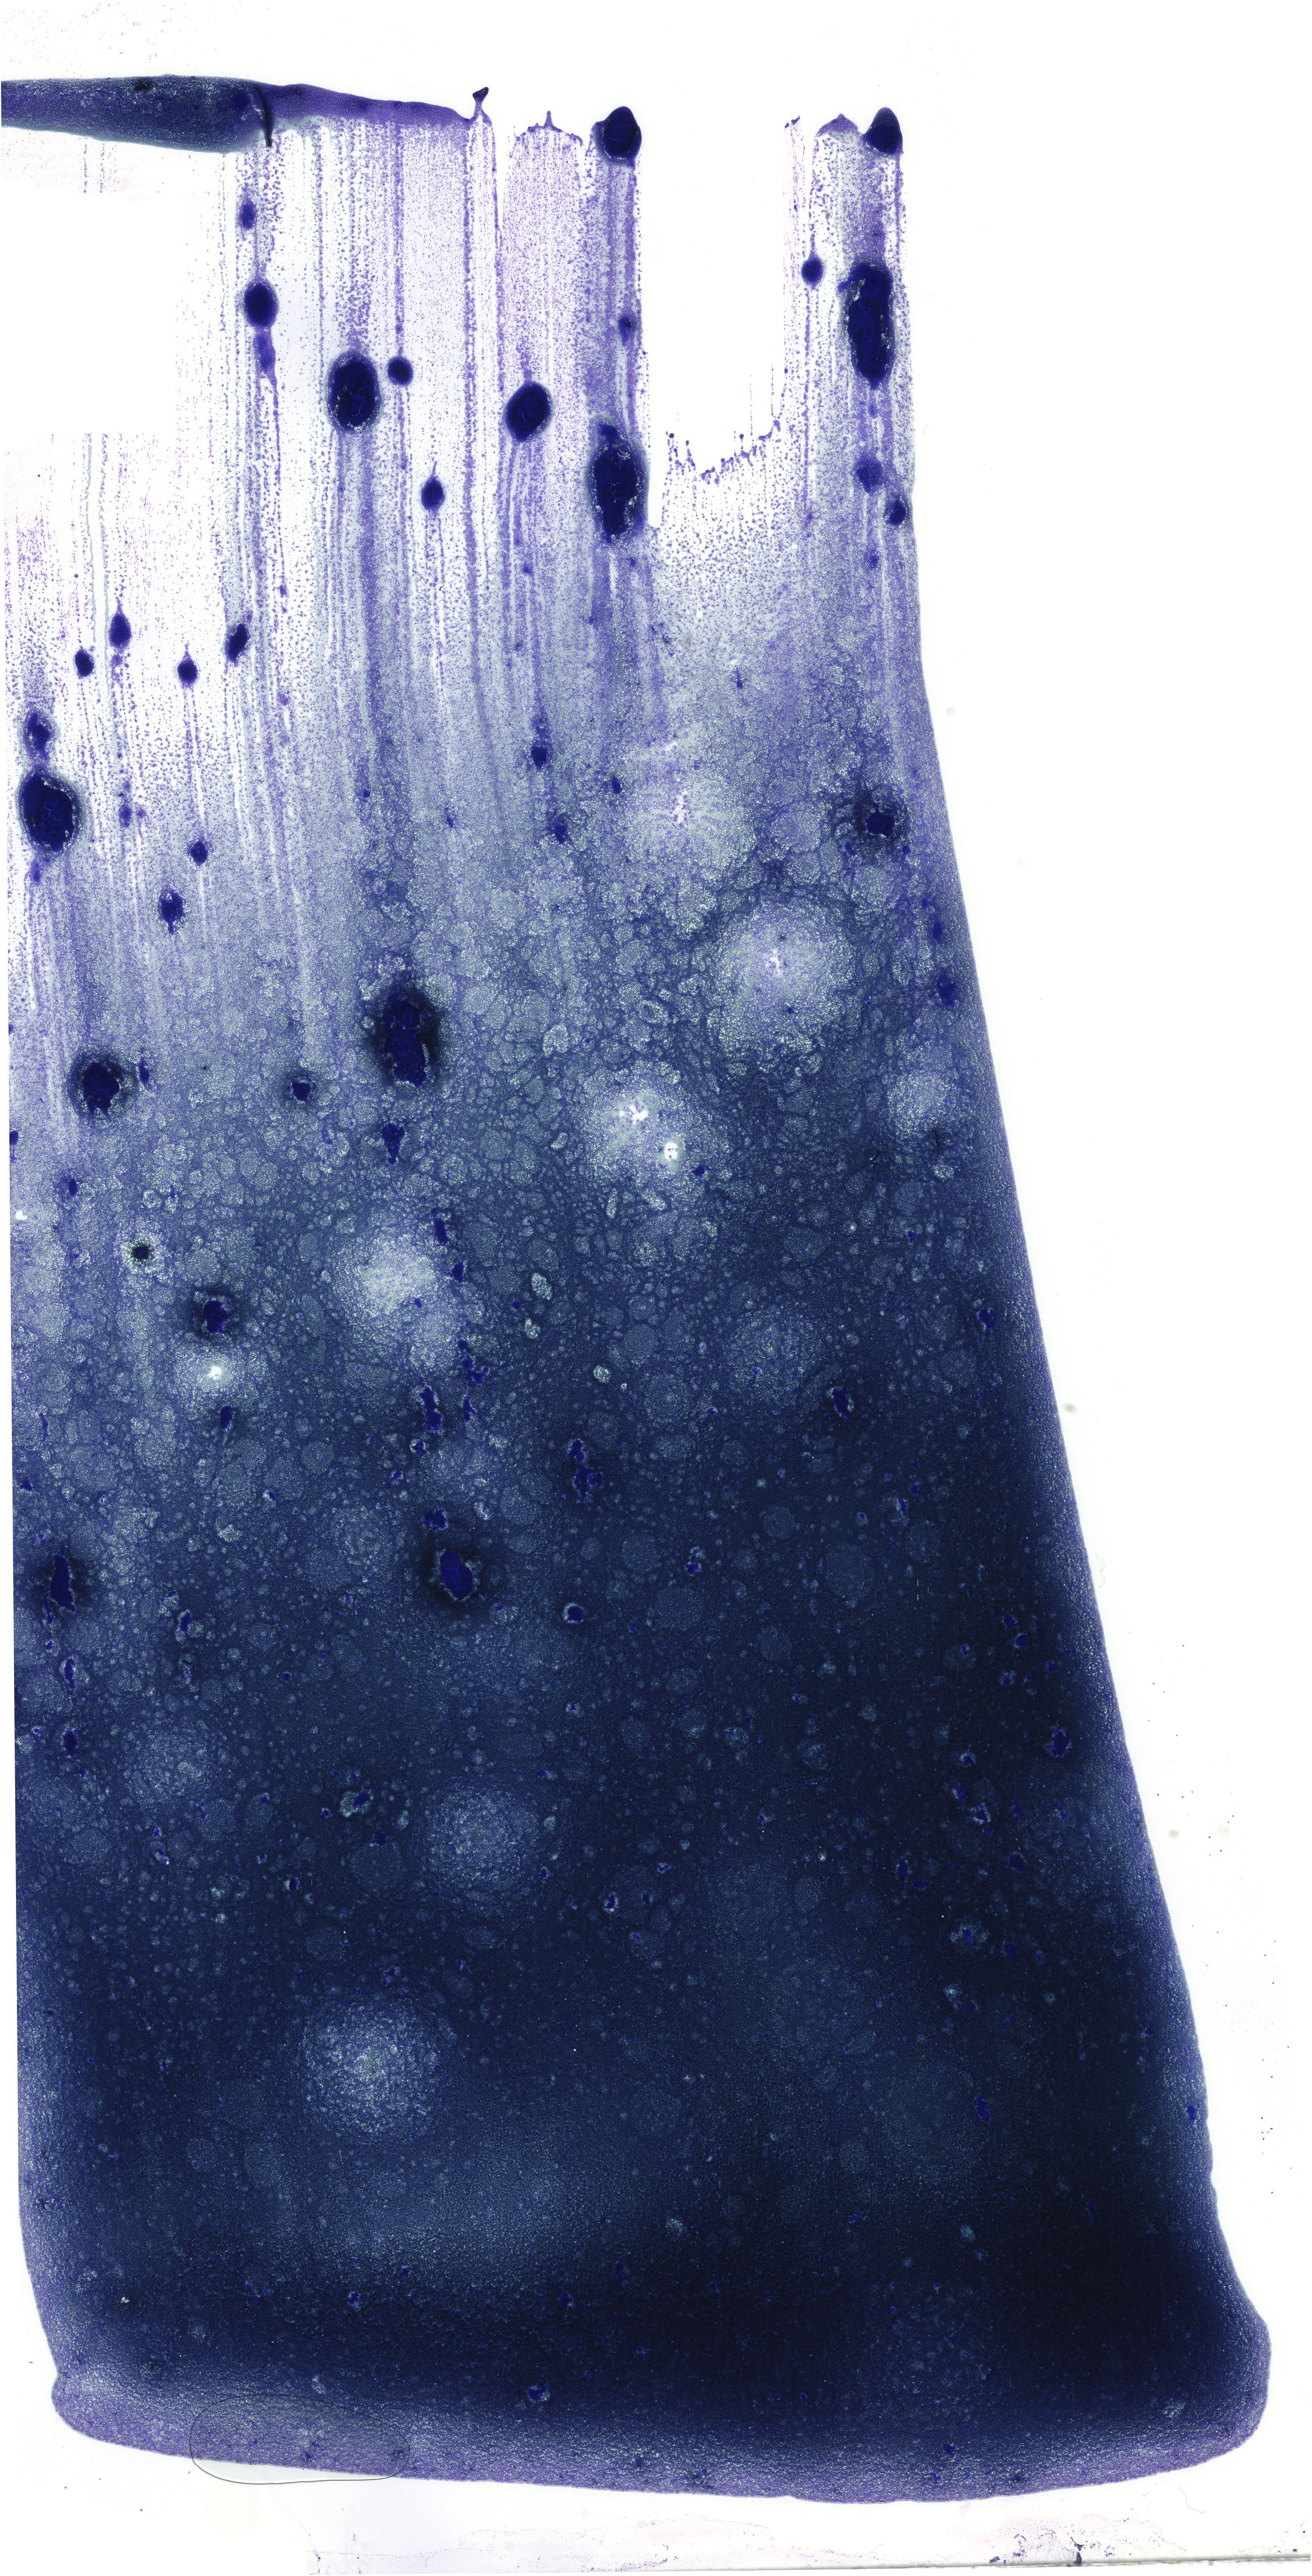
Bone marrow aspirate smear, May-Grünwald-Giemsa (MGG) stain, whole-slide image — low-resolution overview of the scanned area, about 20.9 x 41.0 mm. Patient sex: male.
Diagnosis: Chronic Phase Chronic Myeloid Leukemia, BCR-ABL1 Positive.